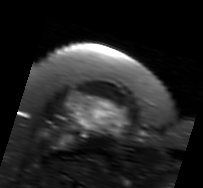
MRI of an extremity soft-tissue mass, one axial slice. Position 62 of 91 along the scan axis. T2-weighted fat-saturated. MR volume resampled by the dataset authors to the PET/CT grid (not the native acquisition matrix). 3.27 mm slice thickness. 203 × 188 image matrix. Female patient. Case-level facts recorded for this patient, not image findings: histological type: malignant solitary fibrous tumor; grade: intermediate; site of the primary tumour: right thigh.
Outlined on this slice (expert contour drawn on MRI and transferred to this co-registered scan by the dataset authors):
- gross tumour volume including surrounding oedema: bounding box [x1, y1, x2, y2] px = [54, 90, 128, 148]
- gross tumour volume (mass): [72, 95, 121, 132]